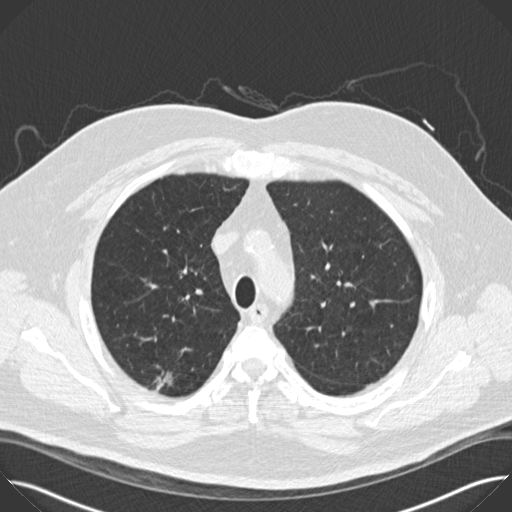
Axial slice from a low-dose chest CT screening exam; baseline annual screen; lung window (W 1500 / L -600 HU); 2 mm slice thickness; slice 122 of 158 in the series. Male participant, aged 65 years at enrolment. Former smoker at enrolment.
• Expert reader's lesion annotation, bounding box [x1, y1, x2, y2] px = [149, 360, 191, 418].
• The screening reader recorded 2 non-calcified nodules or masses ≥4 mm on this exam (right upper lobe, right upper lobe); which of them this box marks is not recorded.
• Later outcome: lung cancer diagnosed 47 days after this screen — bronchiolo-alveolar adenocarcinoma, NOS, right upper lobe, moderately differentiated (G2), stage IIA (AJCC 6th edition), 14 mm at pathology.